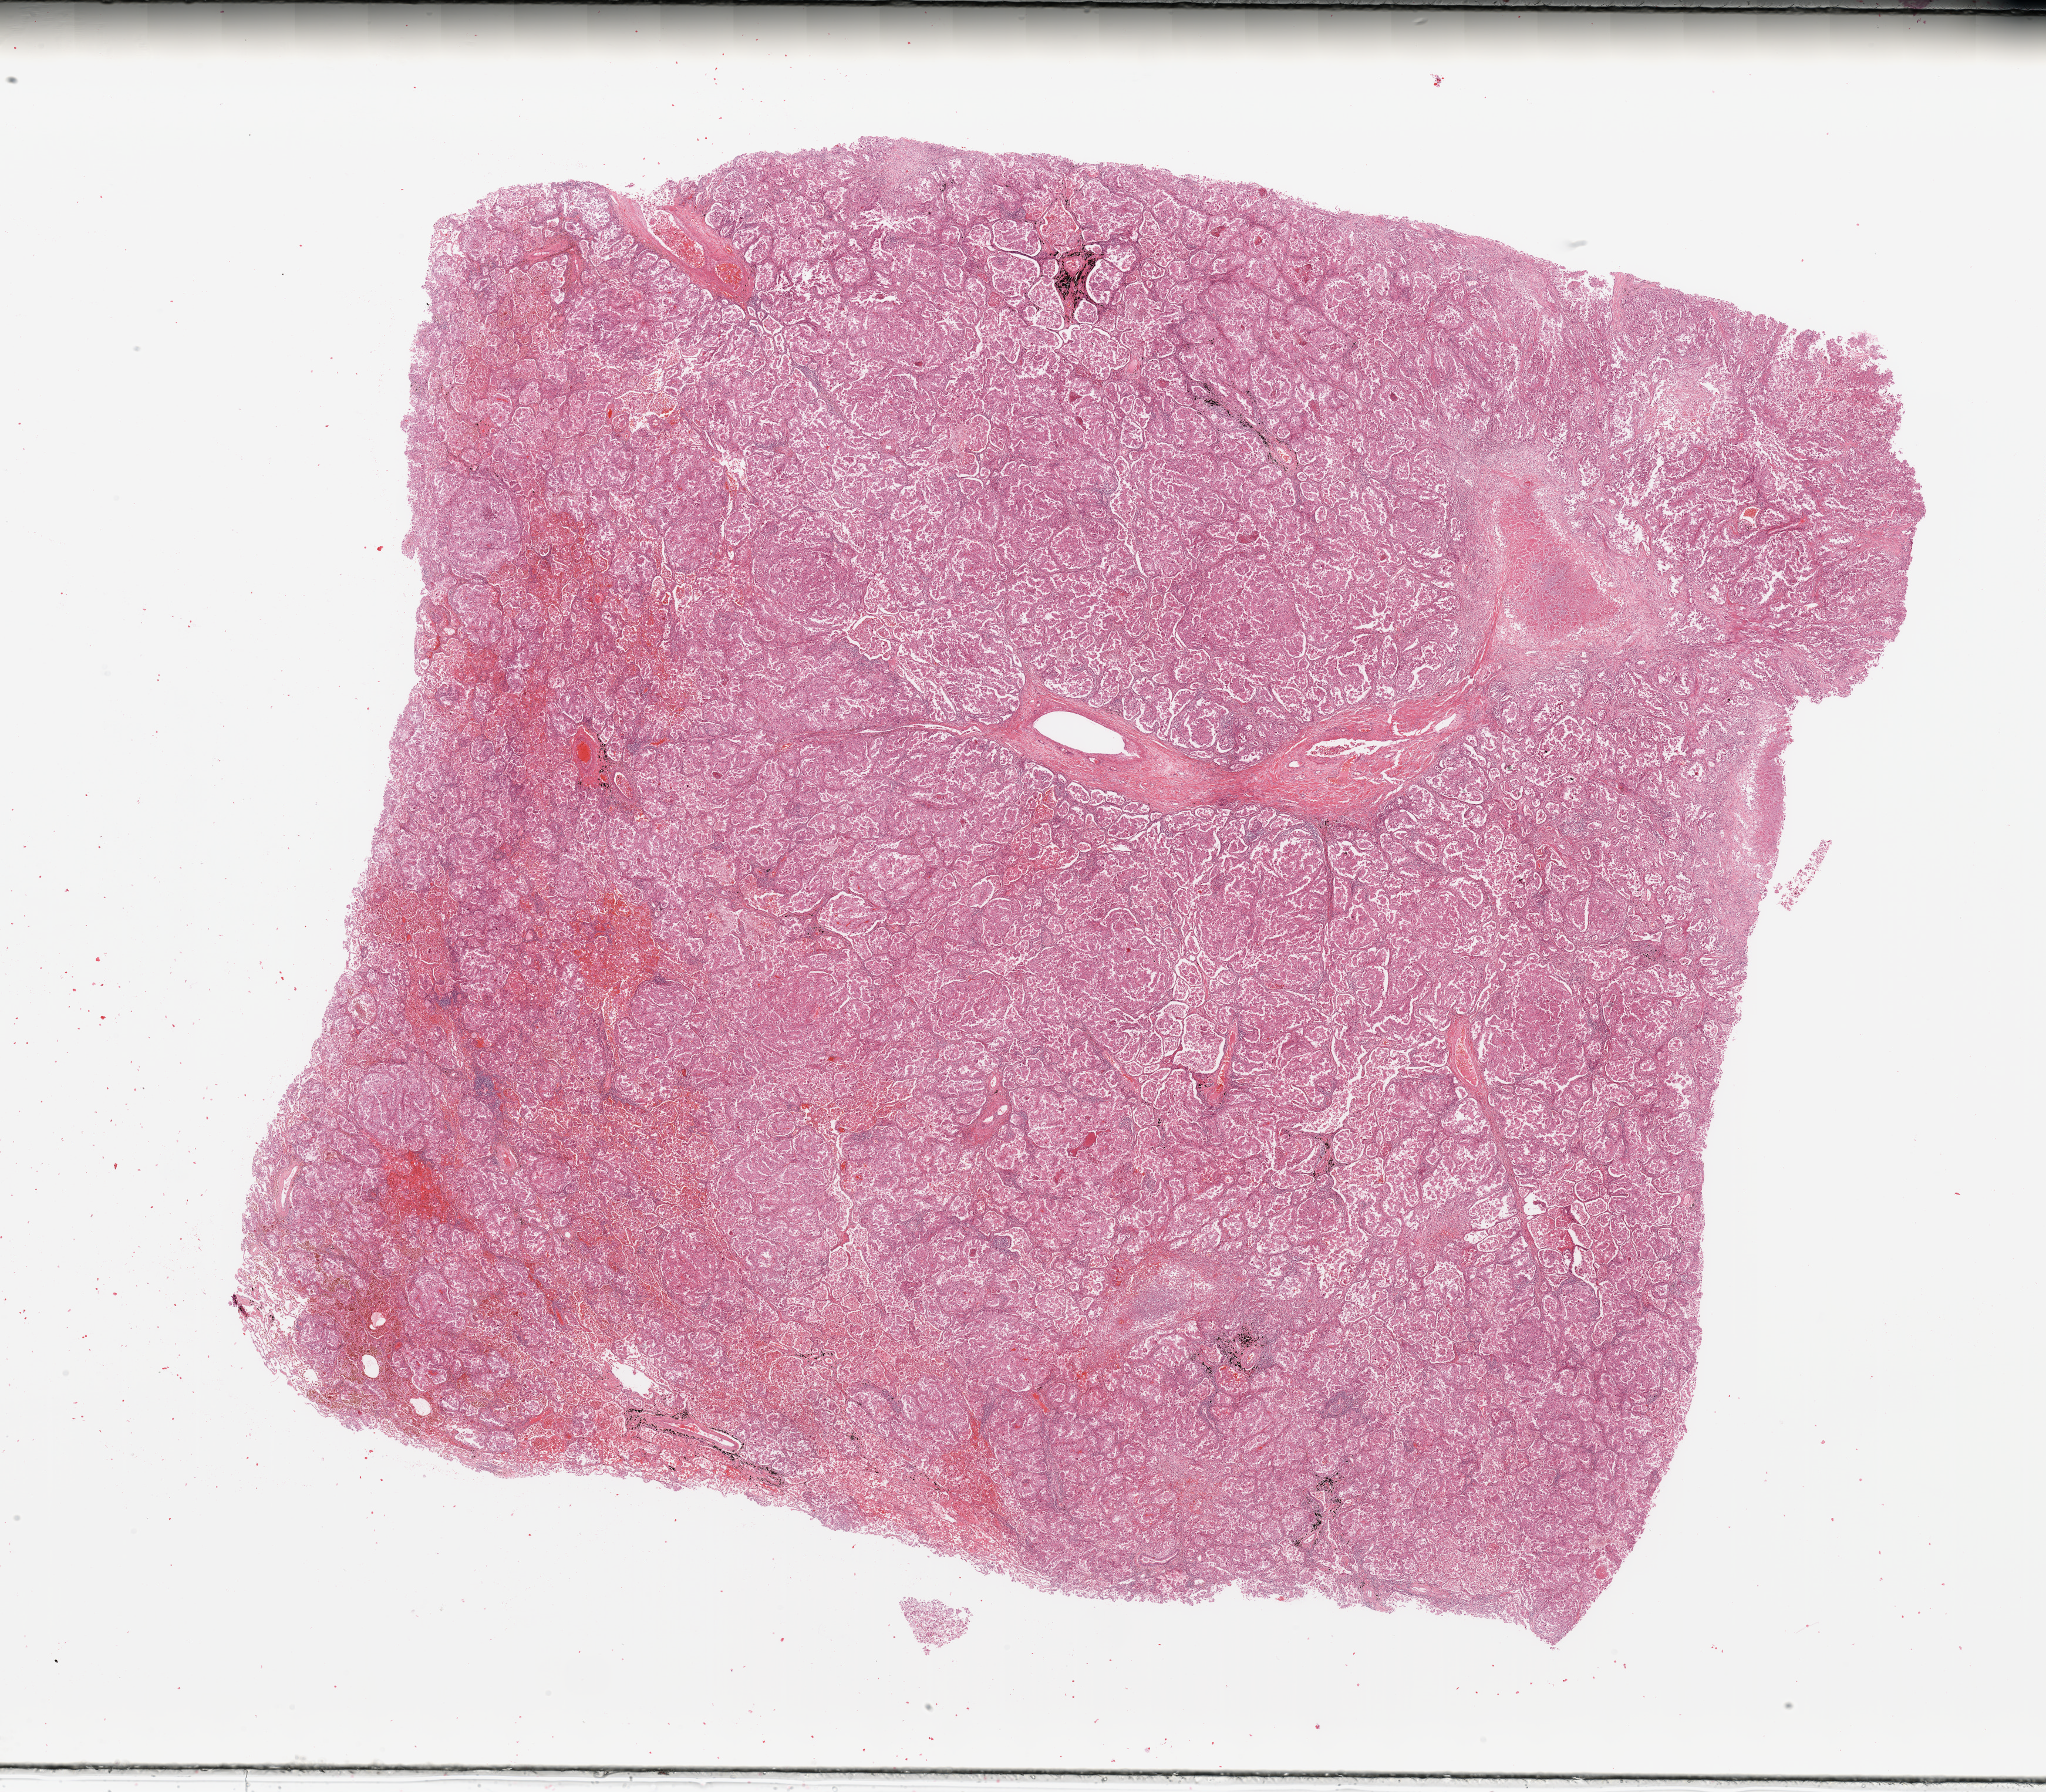
Whole-slide histology image, H&E-stained, a low-resolution overview of the entire scanned area, about 27.6 x 24.1 mm (acquisition: 20x scan). Tumour tissue sample, lung. Male, 55 y/o.
Diagnosis: Adenocarcinoma, NOS.